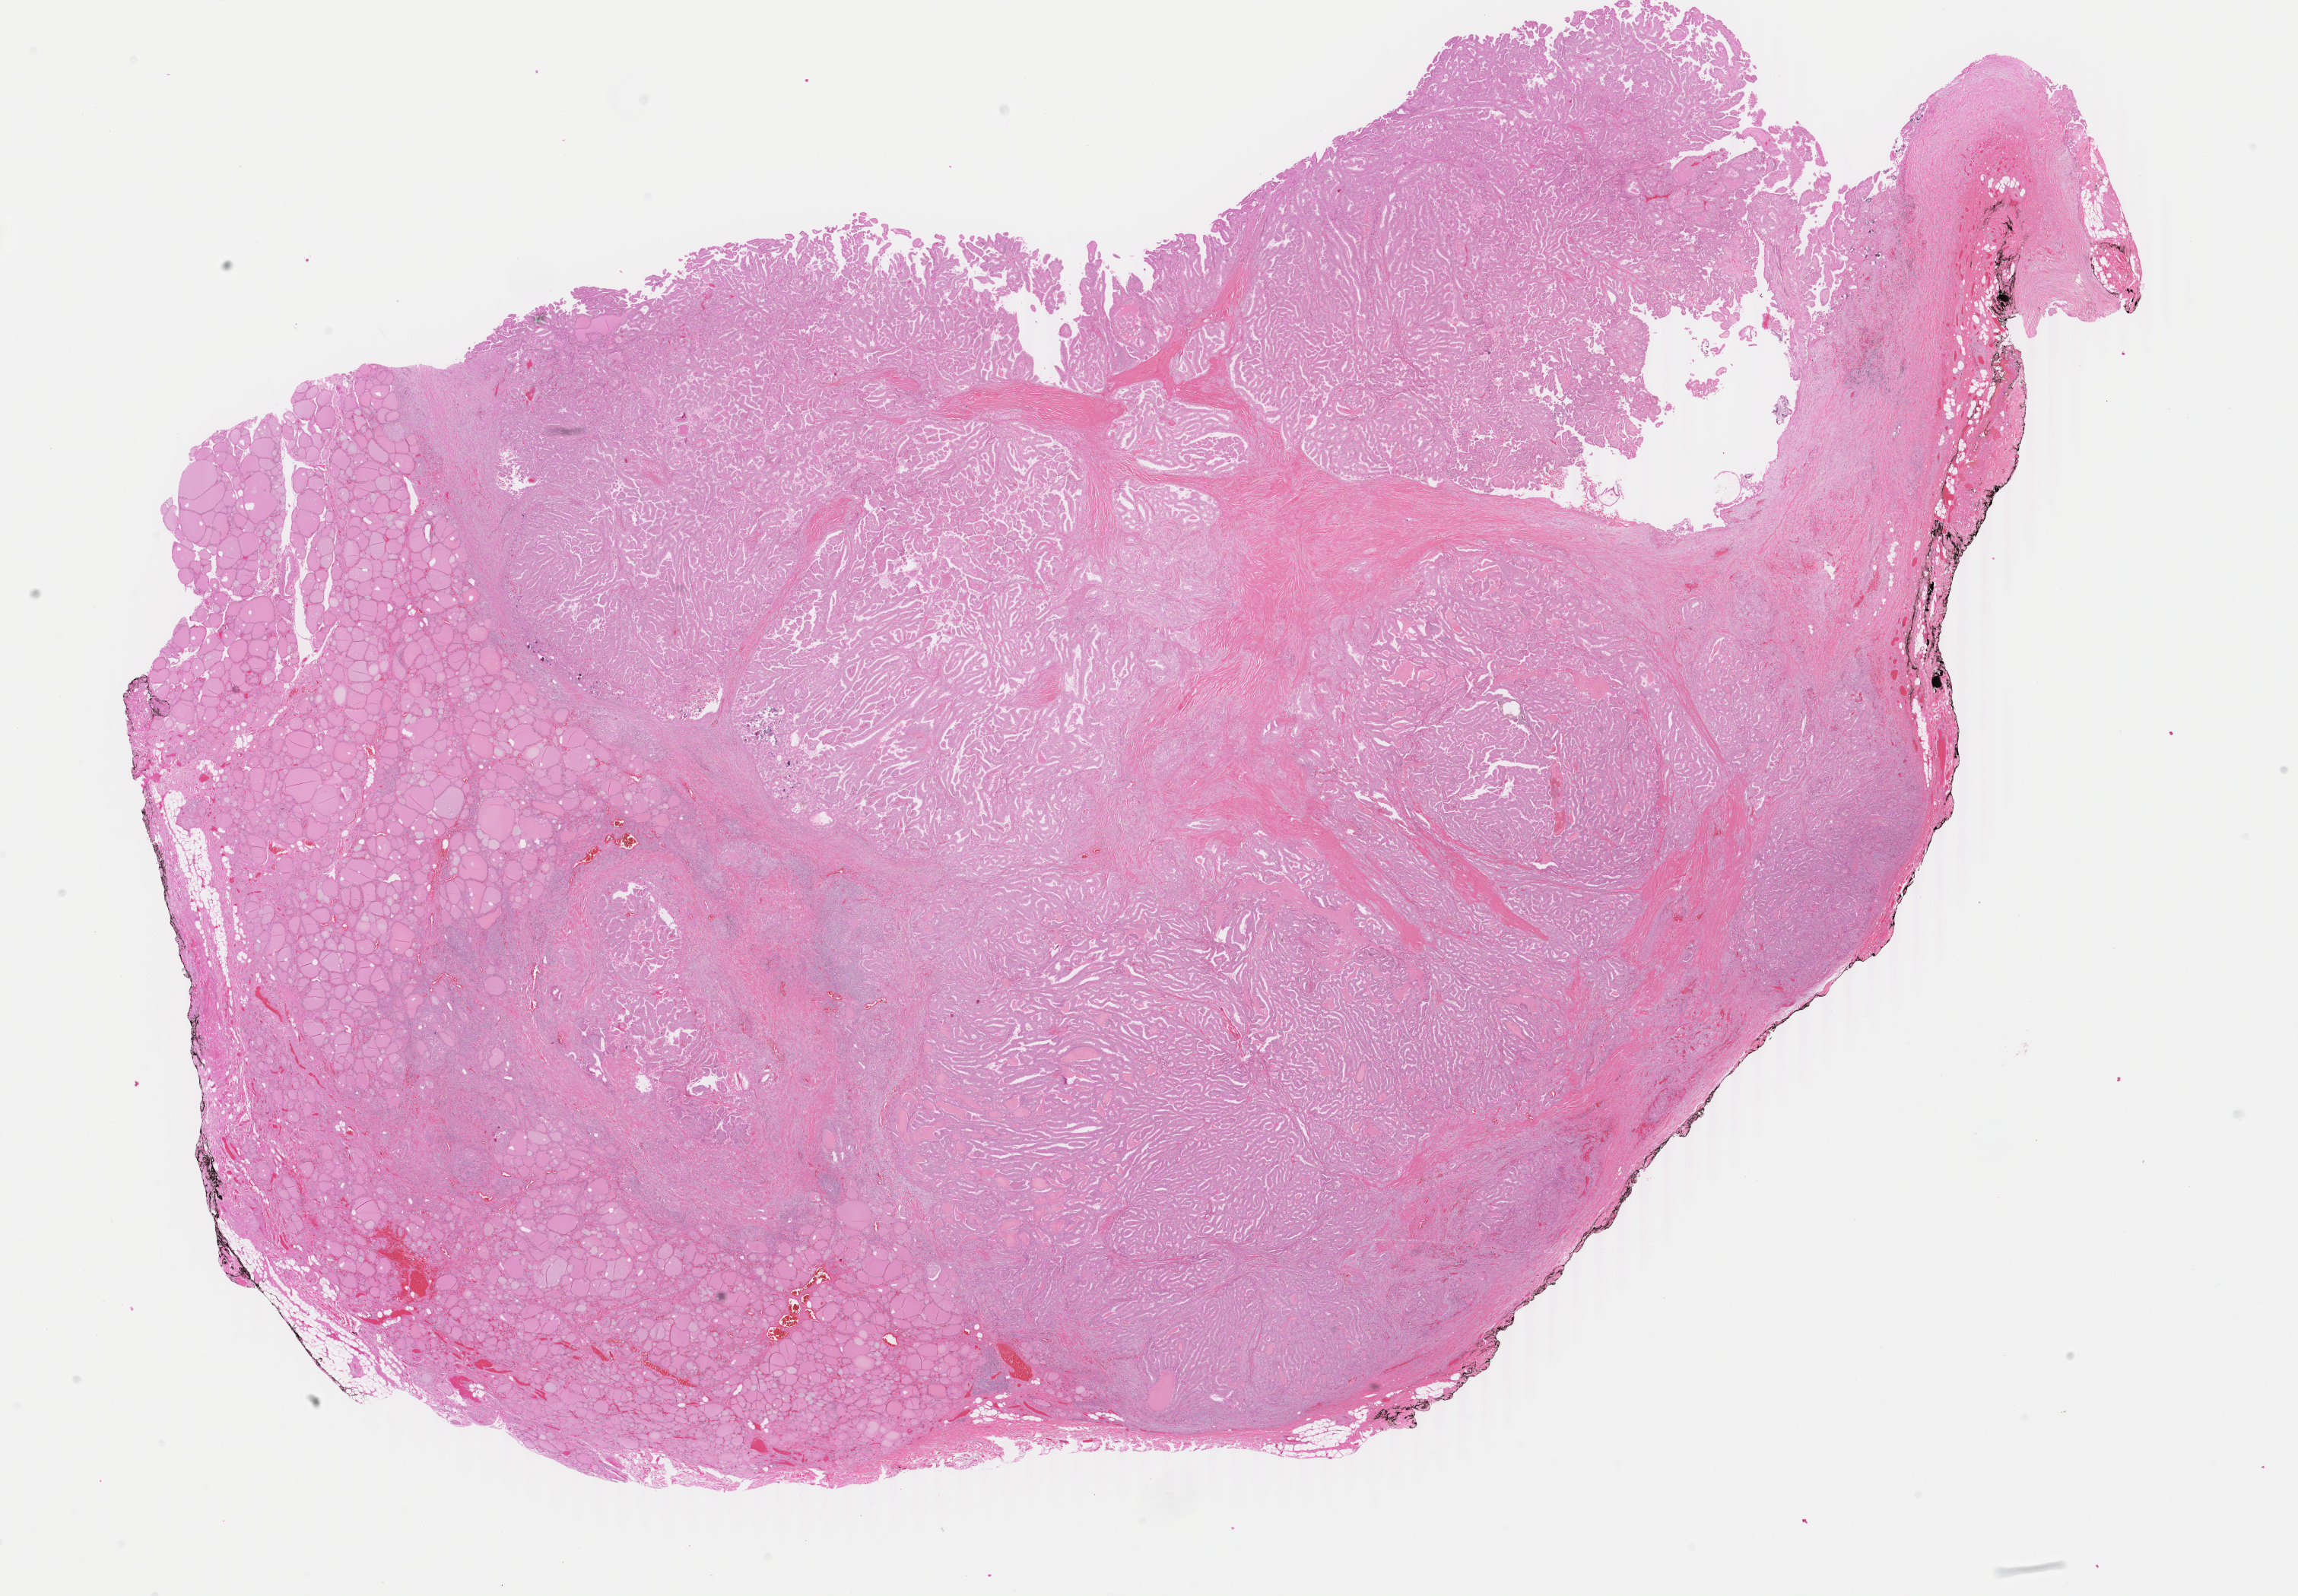
Digitized H&E-stained tissue section (whole slide) — whole scanned area (about 24.0 x 16.7 mm) shown as a low-resolution overview. Formalin-fixed paraffin-embedded (FFPE) diagnostic section. Primary tumour sample from the thyroid. Male patient; age at initial diagnosis 74 years.
AJCC pathologic stage: III (6th edition). Histologic diagnosis: Papillary adenocarcinoma, NOS. Lymph nodes positive (case pathology): 0 of 1 examined.